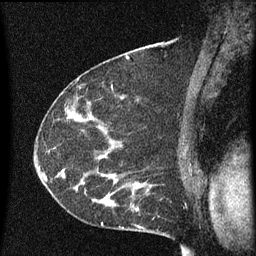
Breast MRI (dynamic contrast-enhanced), one sagittal slice; position 39 of 60 along the scan axis; dynamic contrast-enhanced series, image 2 of 3 at this slice position (ordered by acquisition); 1.5 T; TE 4.2 ms, TR 8 ms; 2 mm slice thickness; 256 × 256 image matrix, field of view 180 × 180 mm. Female patient, age 55 years.
Annotated regions visible in this slice (semi-automatically segmented with operator editing):
- analysis volume of interest (the breast-tissue region the enhancement analysis was run in; not a lesion): bounding box [x1, y1, x2, y2] px = [51, 156, 145, 217]
- tumour enhancement mask (voxels above the 70 % enhancement threshold inside the analysis volume of interest): [62, 156, 143, 211]